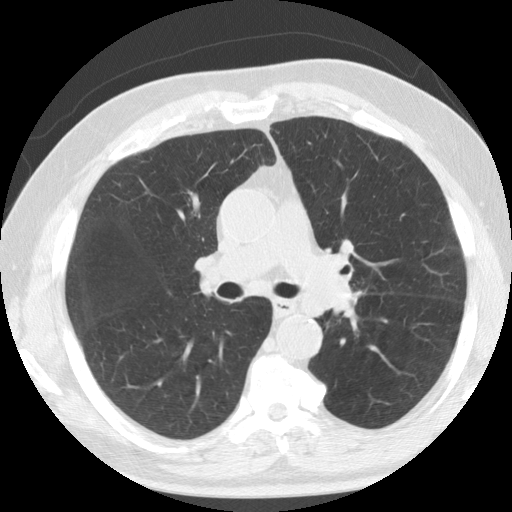
Low-dose screening chest CT, one axial slice. Position 81 of 133 along the scan axis. Reconstruction kernel STANDARD. Lung window (W 1500 / L -600 HU). 2.5 mm slice thickness. 512 × 512 image matrix, field of view 342 × 342 mm.
Annotated regions visible in this slice (outlined manually by an expert reader):
- lesion 1 (tumor, upper lobe of left lung): bounding box [x1, y1, x2, y2] px = [310, 262, 352, 314]